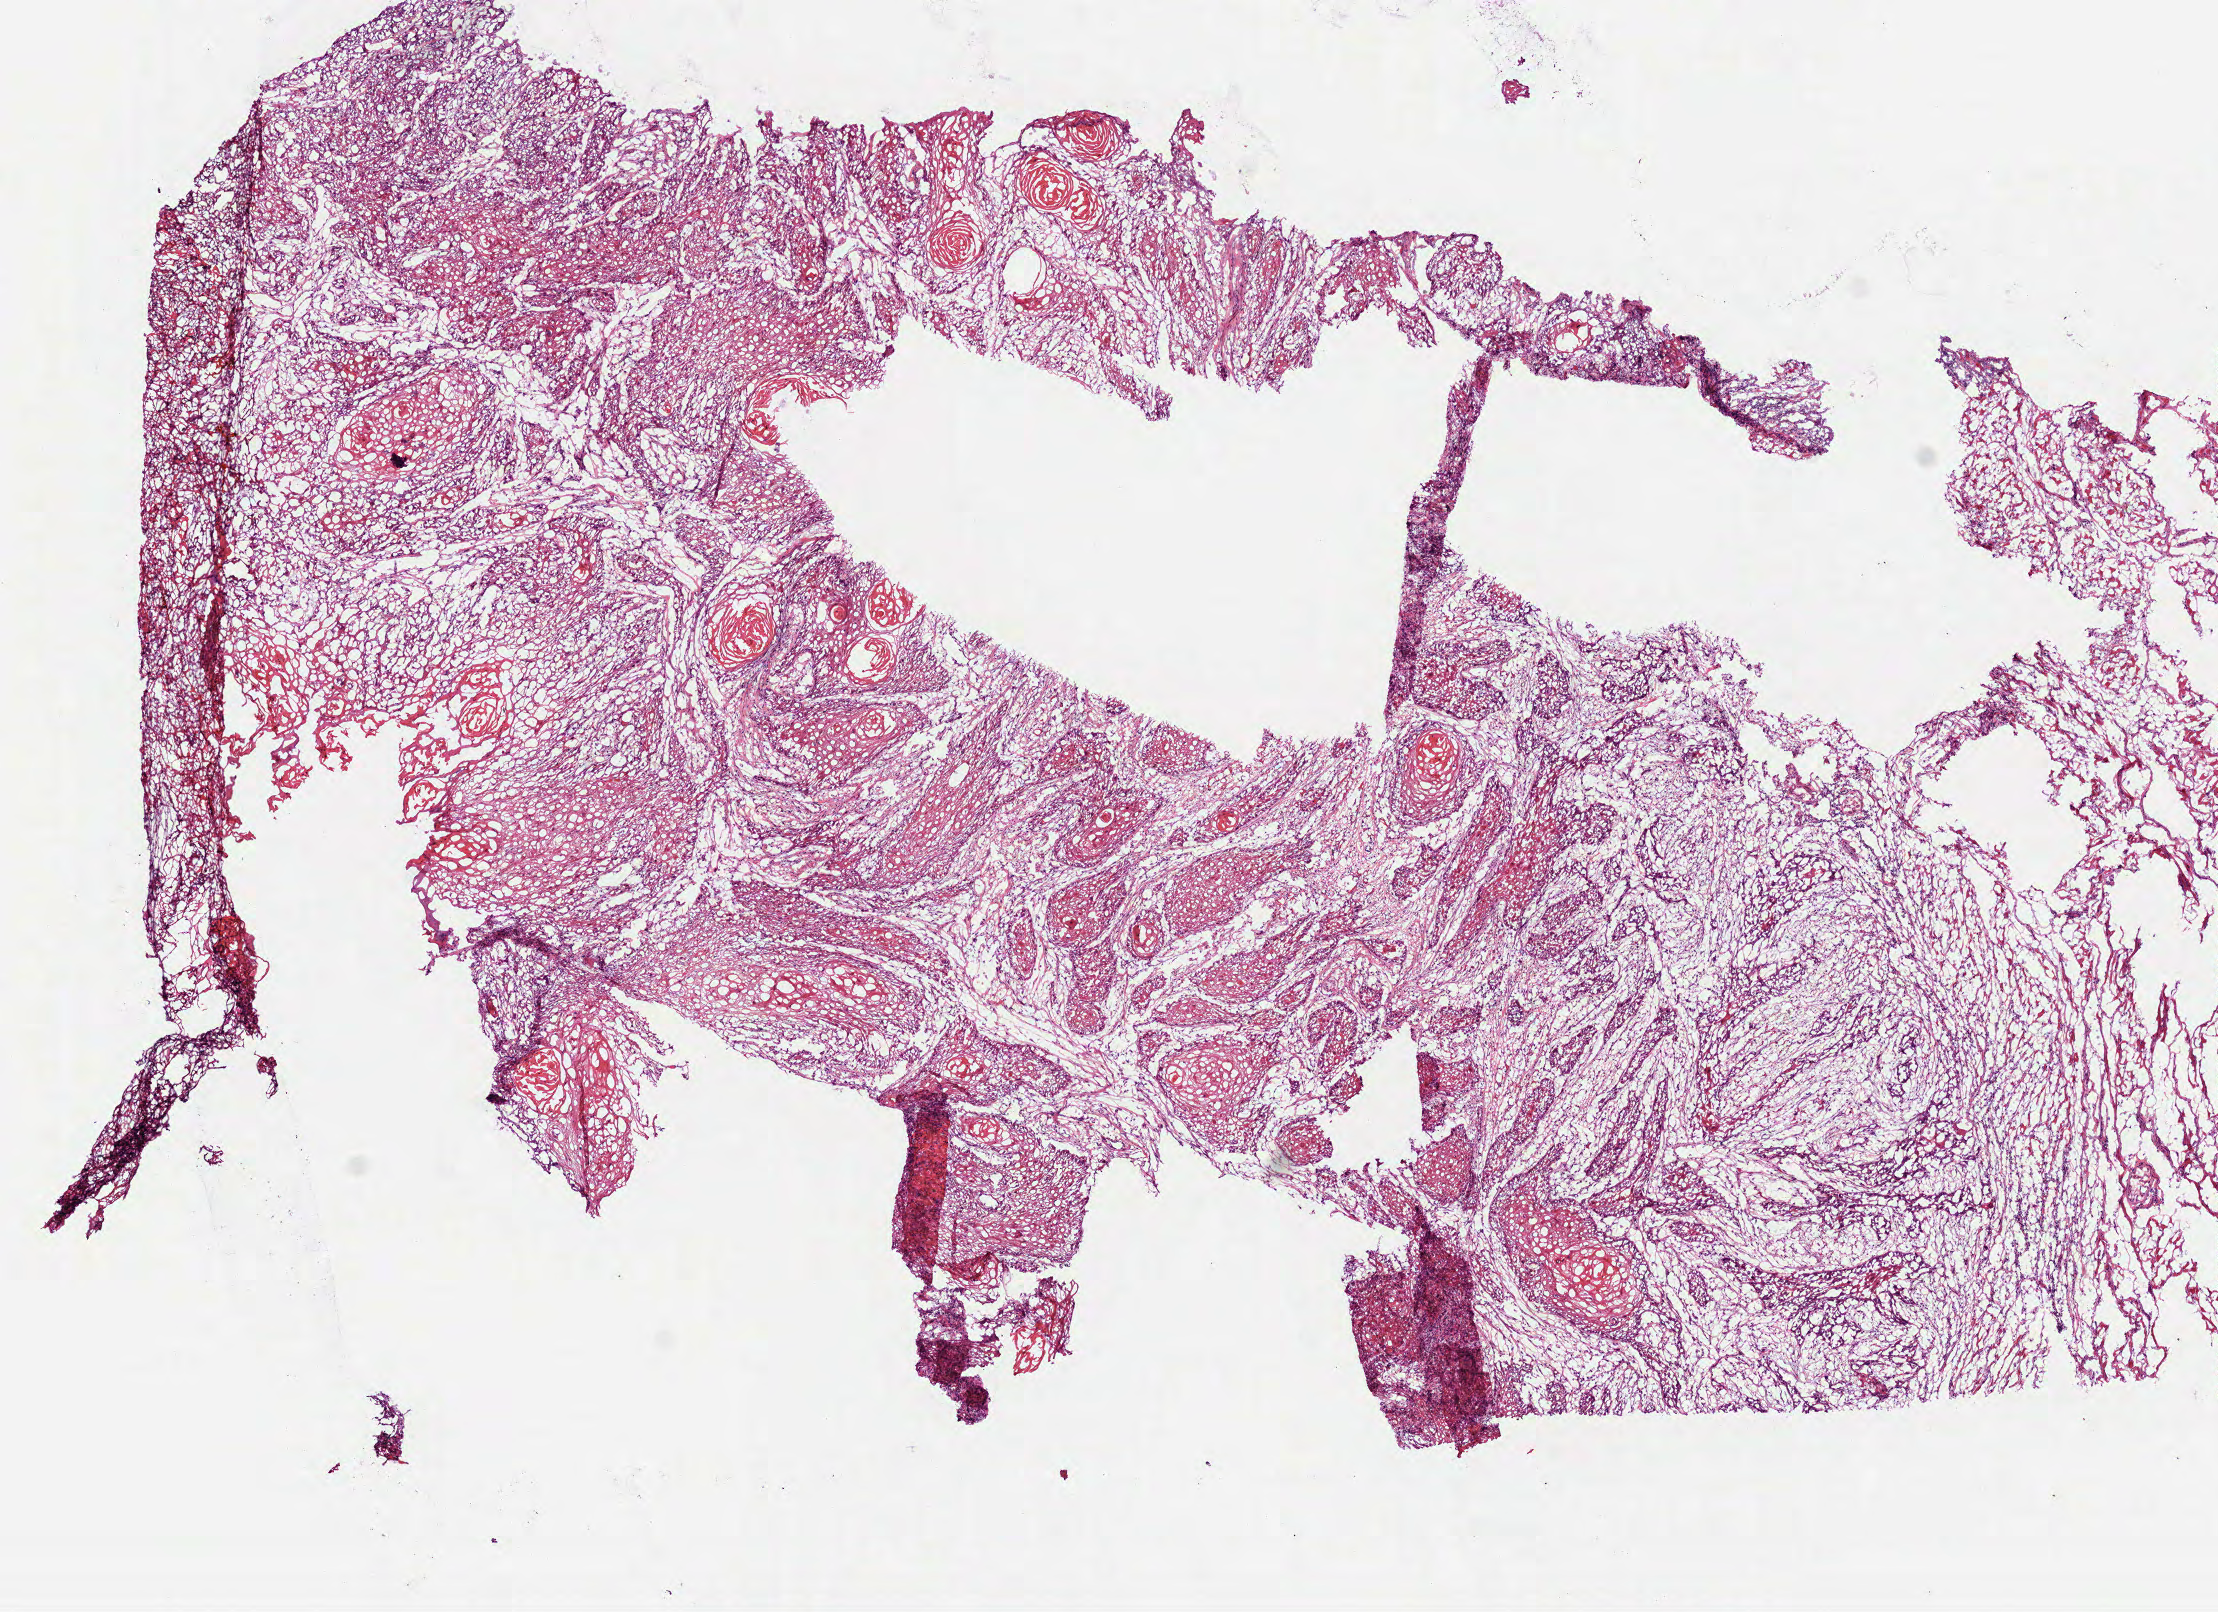
H&E-stained whole-slide image, shown as a low-resolution overview of the whole scanned area (about 8.9 x 6.5 mm), frozen section from the top of the tissue portion, sample: primary tumour, head and neck. Male patient; age at initial diagnosis 50 years. Slide review estimates, as recorded: tumour cells 80%, tumour nuclei 70%.
Histologic diagnosis: Squamous cell carcinoma, NOS (tongue, NOS).